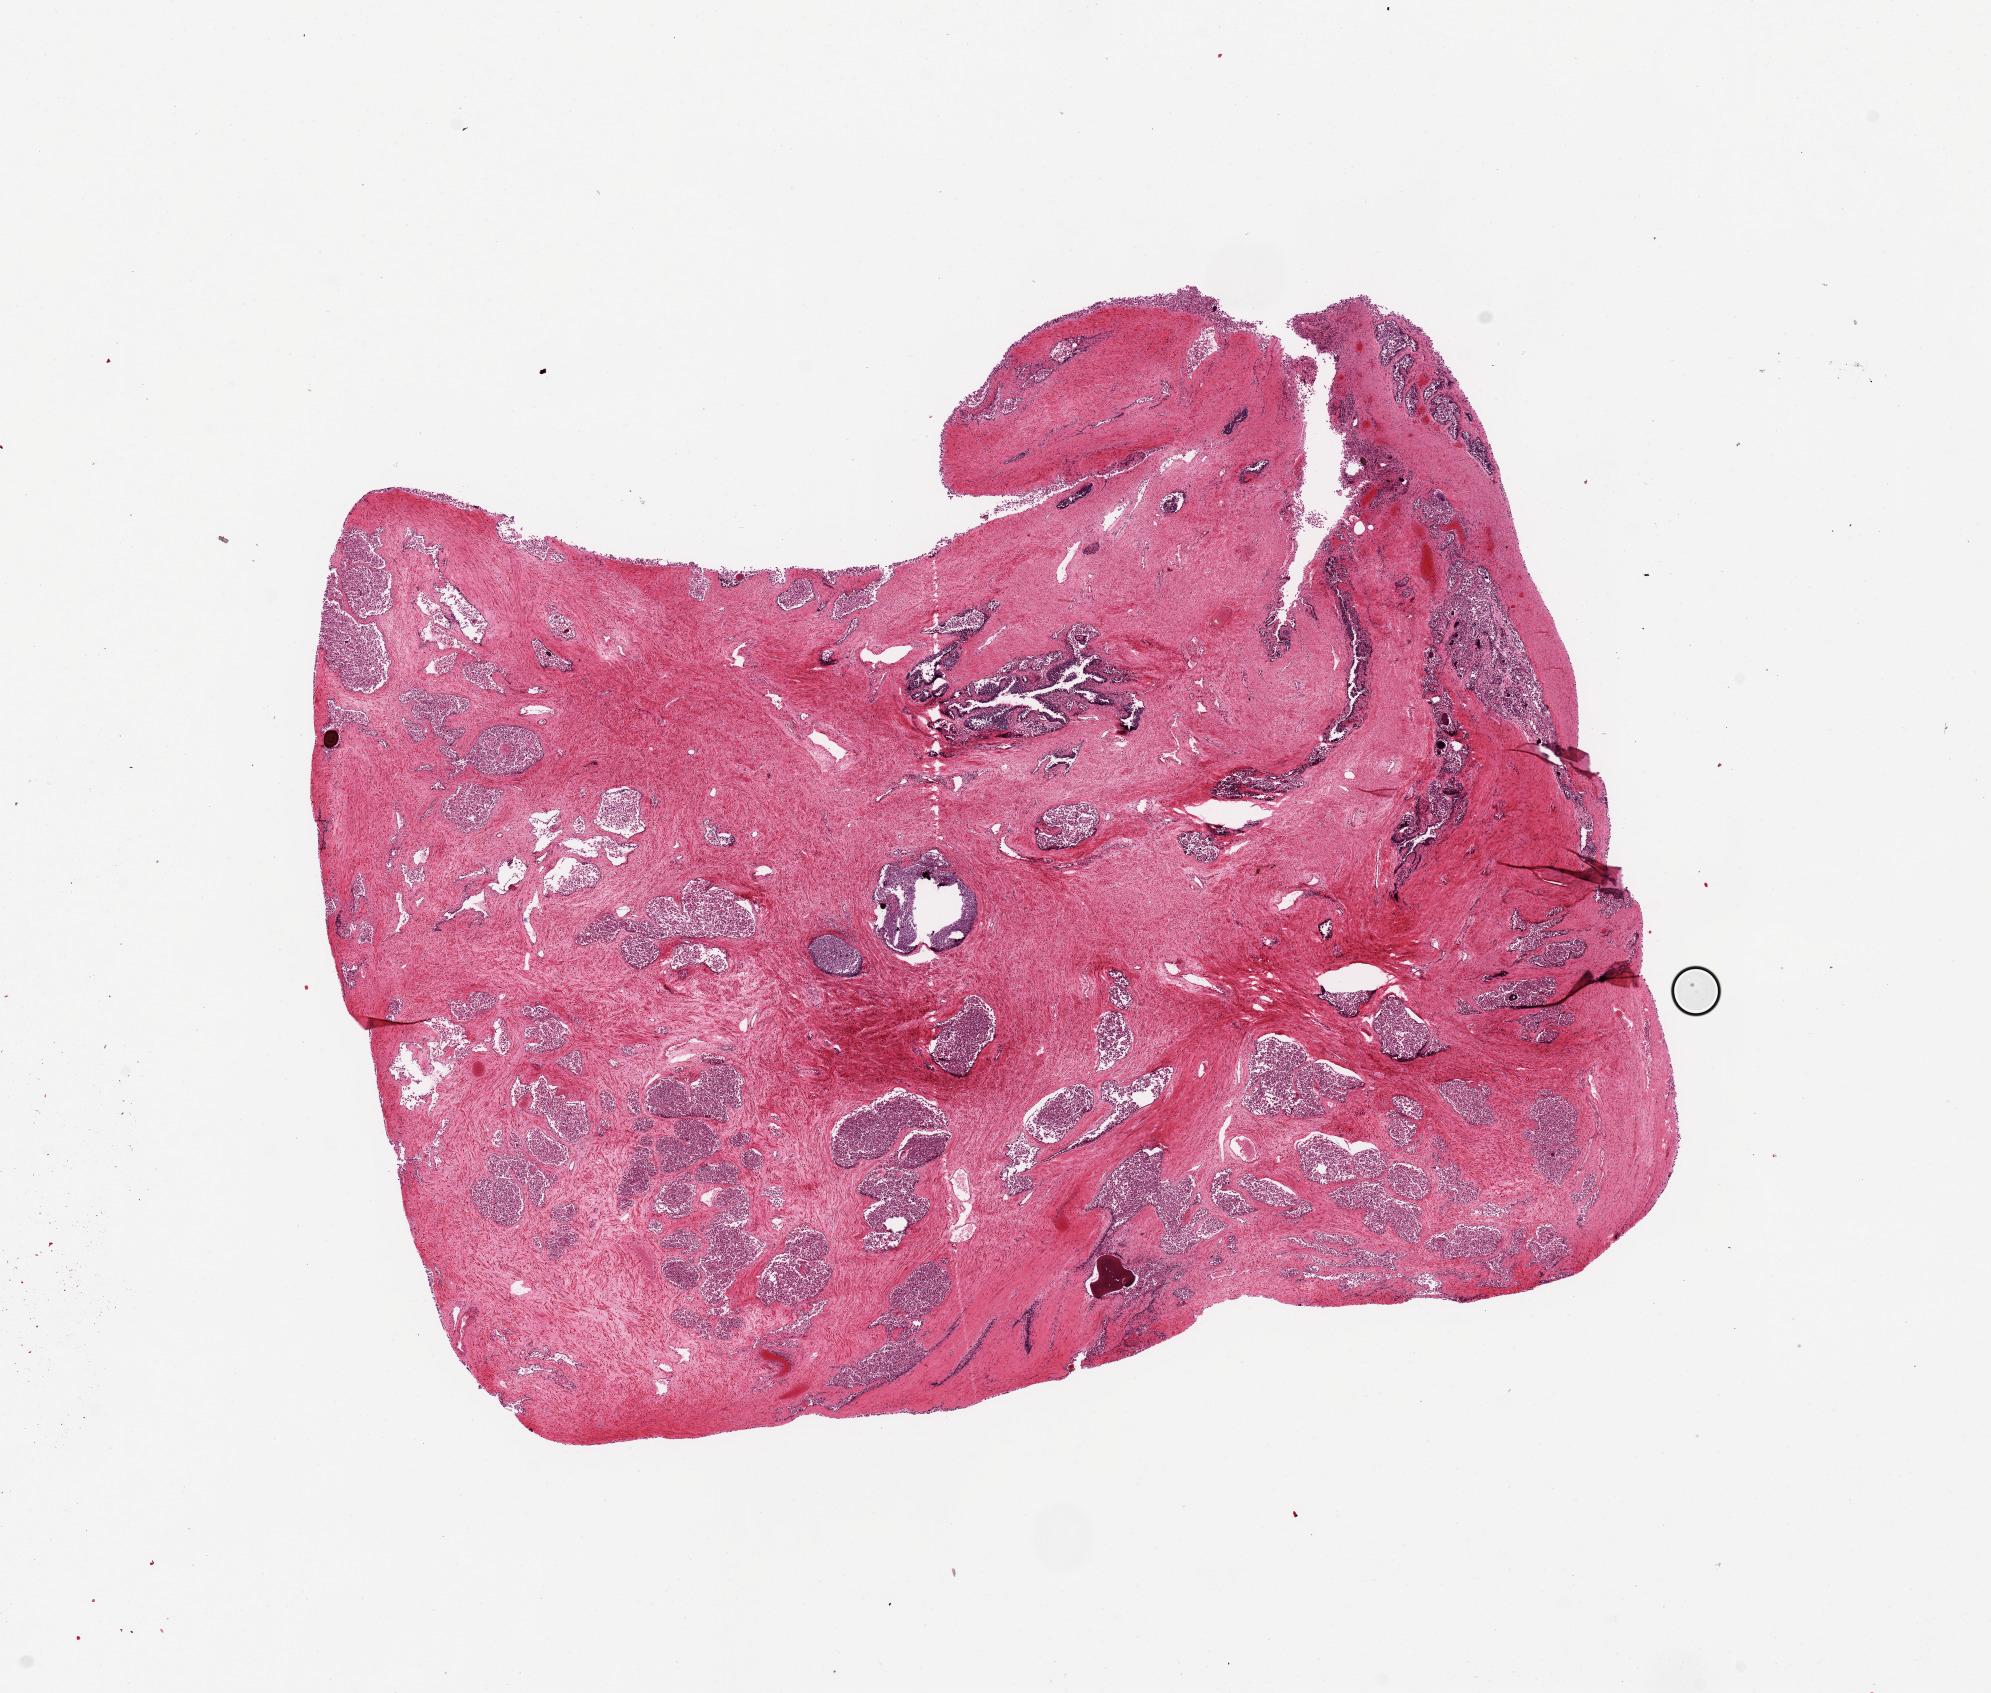
Whole-slide image, H&E stain — shown as a low-resolution overview of the whole scanned area (about 15.8 x 13.4 mm, acquisition: 20x scan). PAXgene-fixed paraffin-embedded (PFPE) section. Sampled site (target tissue): prostate. Tissue donor sample. Donor: male.
Pathologist's review note for this sample: Glands ~80% autolyzed.